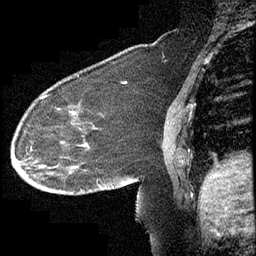
Breast MRI (dynamic contrast-enhanced), one sagittal slice; slice 153 of 232 in the series (ordered by position); dynamic contrast-enhanced study with each time point stored as its own series, time point 2 of 4 at this slice position (early post-contrast, ordered by acquisition time); 1.5 T; TE 4.2 ms, TR 6.7 ms; 3 mm slice thickness; 256 × 256 image matrix, field of view 200 × 200 mm. Female patient, age 63 years. Case-level facts recorded for this patient, not image findings: setting: breast cancer imaged before/during neoadjuvant chemotherapy; receptor status: triple-negative.
Outlined on this slice (semi-automatically segmented with operator editing):
- analysis volume of interest (the breast-tissue region the enhancement analysis was run in; not a lesion): bounding box <13,90,140,211> (left, top, right, bottom; pixels)
- tumour enhancement mask (voxels above the 70 % enhancement threshold inside the analysis volume of interest): <42,95,75,167>